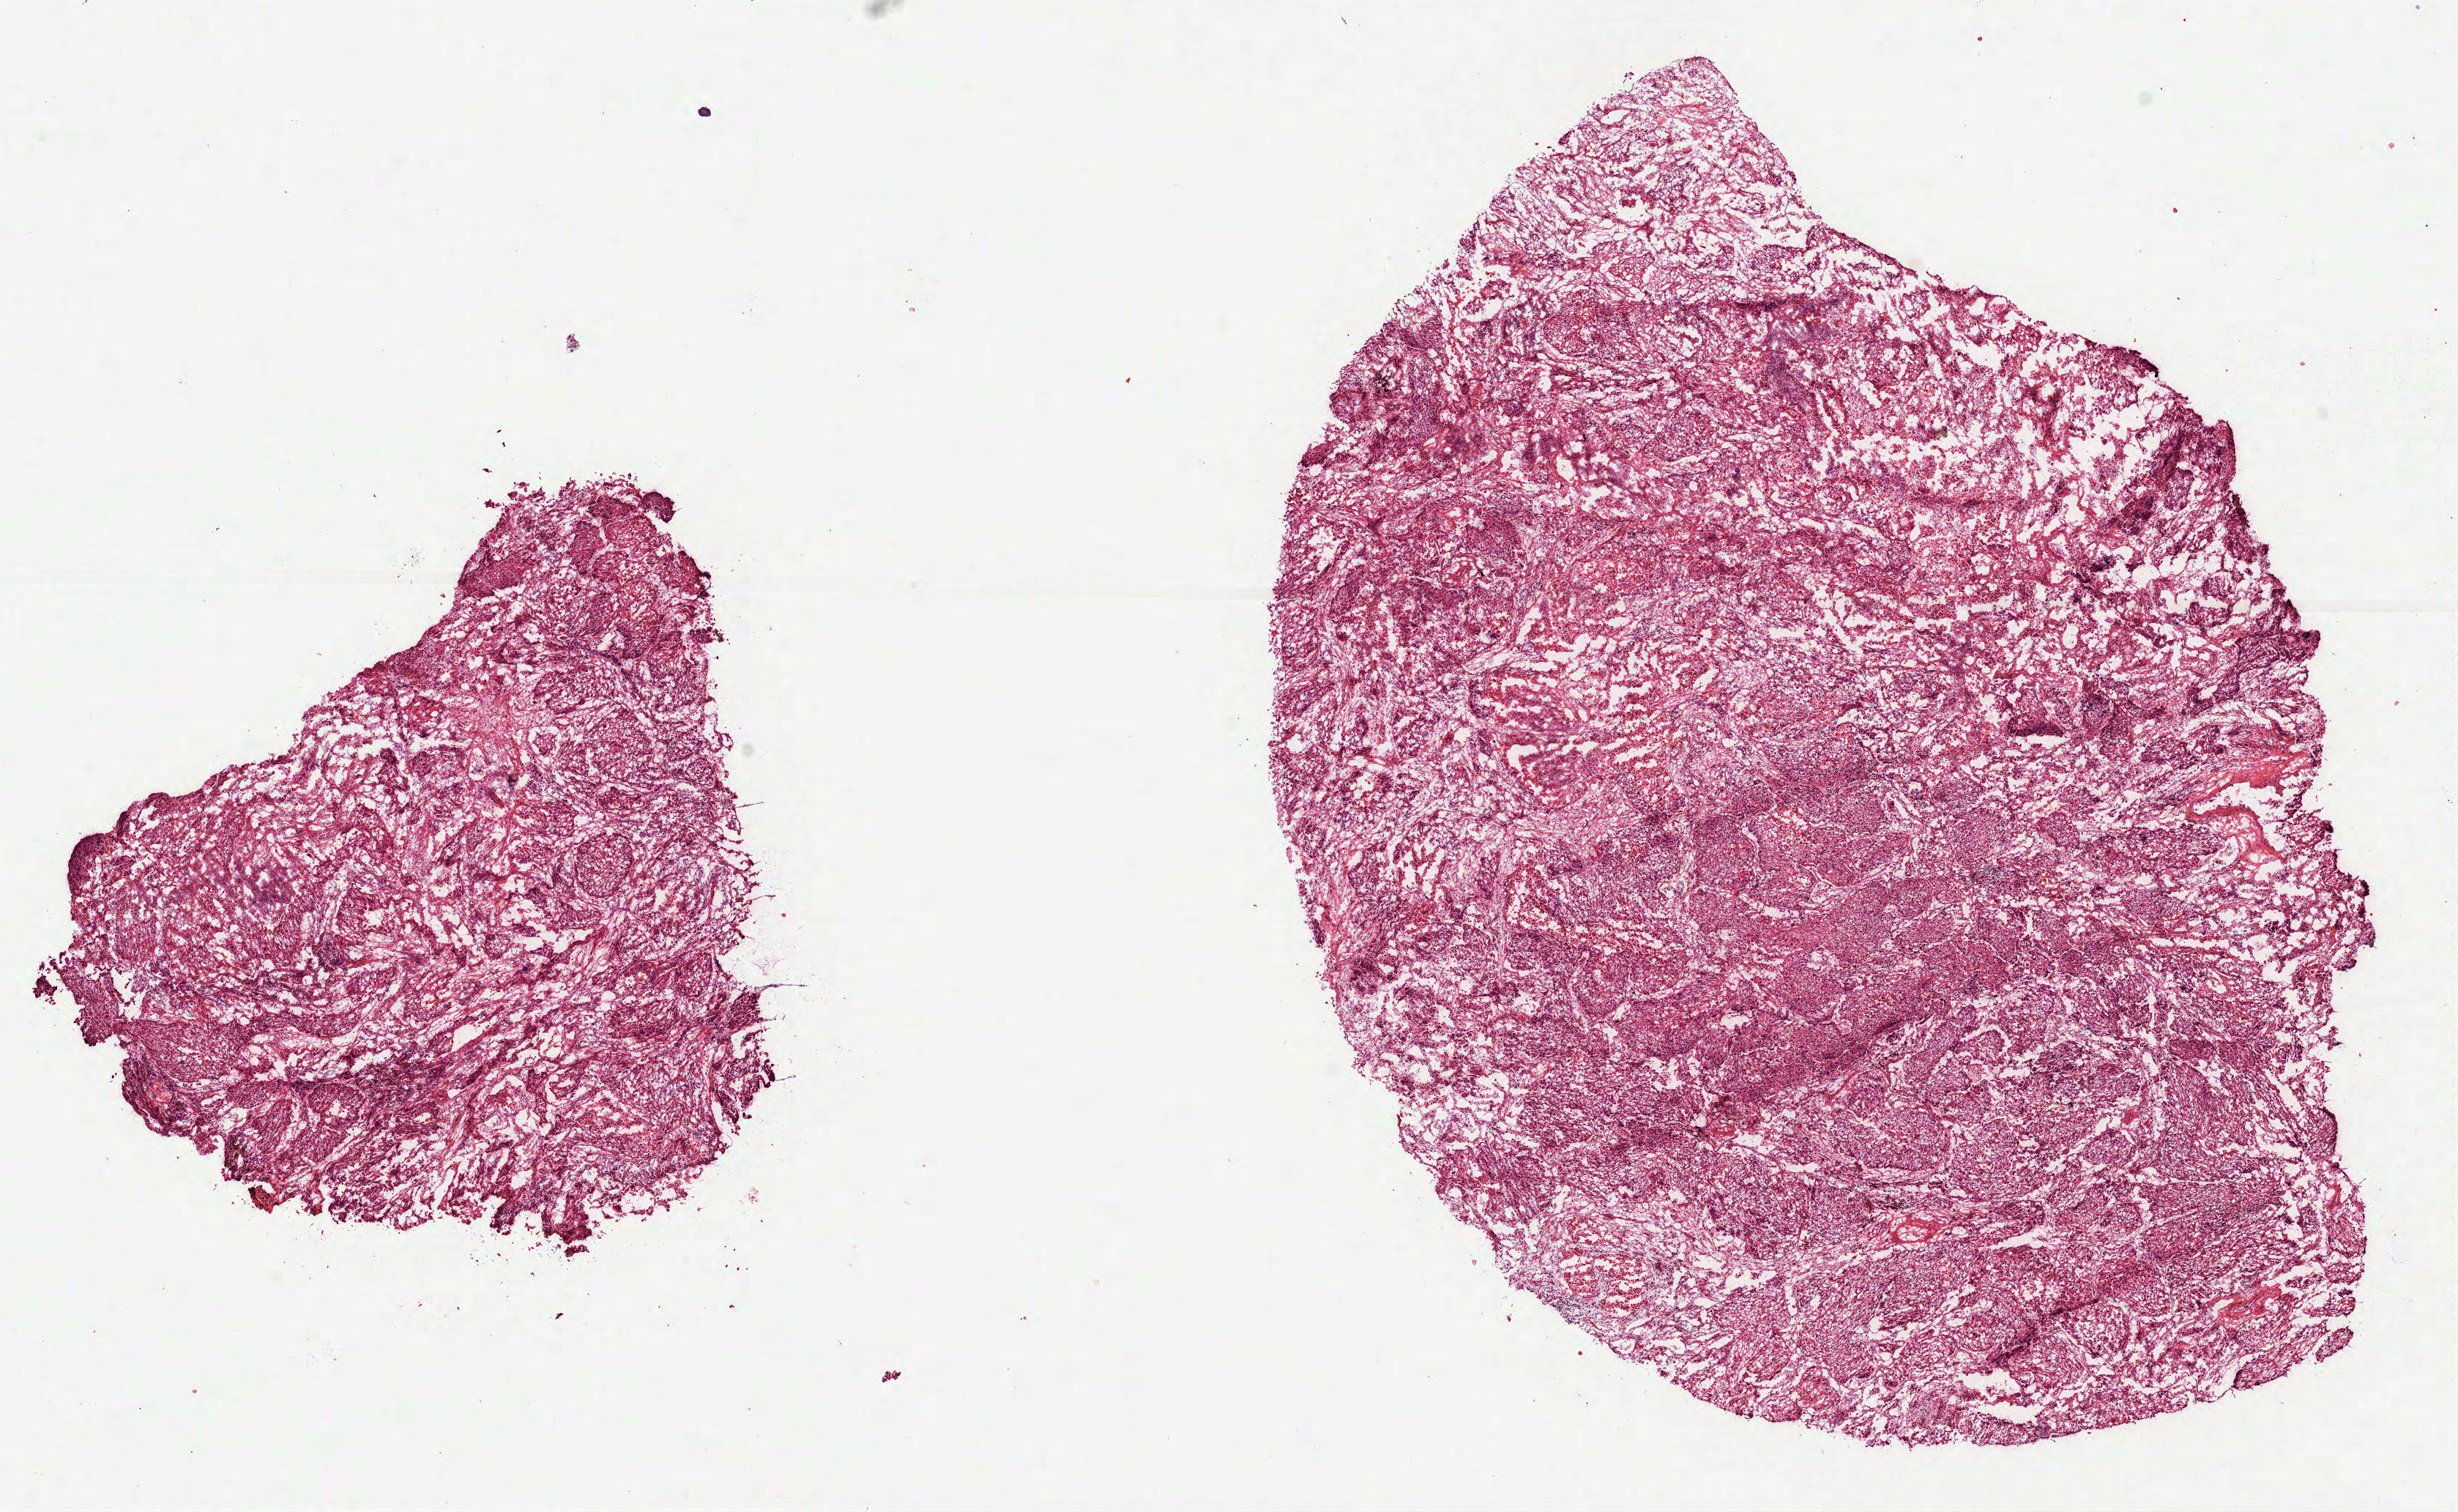
Whole-slide histology image, H&E-stained — whole scanned area (about 13.5 x 8.3 mm) shown as a low-resolution overview. FFPE section. Primary tumour sample from the lung. Male patient; age at initial diagnosis 73 years.
• histologic diagnosis: Squamous cell carcinoma, NOS
• TNM: T2 N0 MX
• AJCC pathologic stage: IB